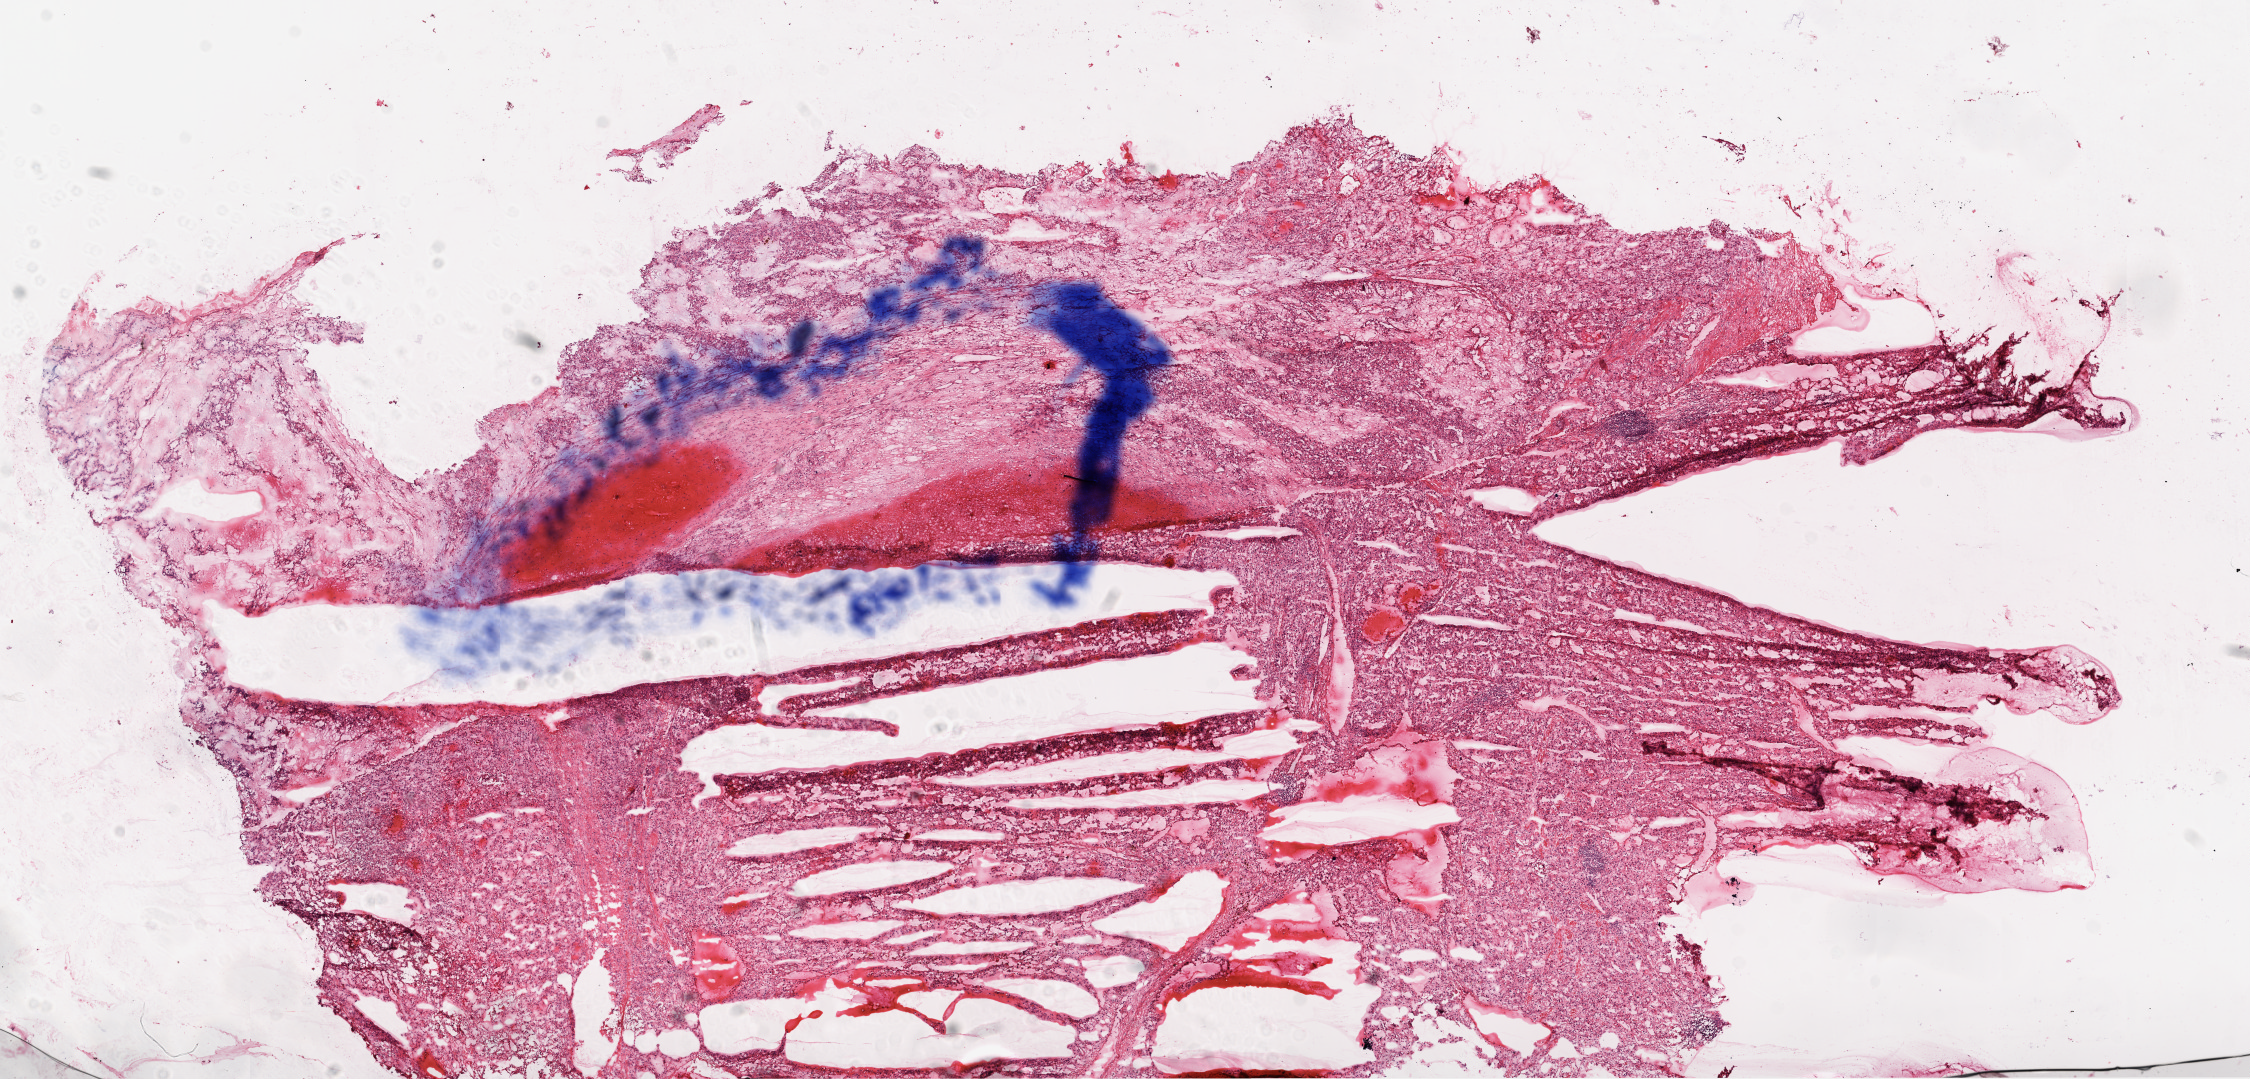
Digitized Hematoxylin and eosin (H&E) stained tissue section (whole slide) — a low-resolution overview of the entire scanned area, about 18.1 x 8.7 mm (slide scanned at 20x), frozen section from the top of the tissue portion, primary tumour sample from the kidney. Male, age 81 years at initial diagnosis. Histologic grade: G3 (poorly differentiated). Pathologist review of this section (percent, as recorded): tumour cells 75%, tumour nuclei 85%, normal cells 0%, stromal cells 25%, necrosis 0%.
Histologic diagnosis: Clear cell adenocarcinoma, NOS. AJCC pathologic stage: III.